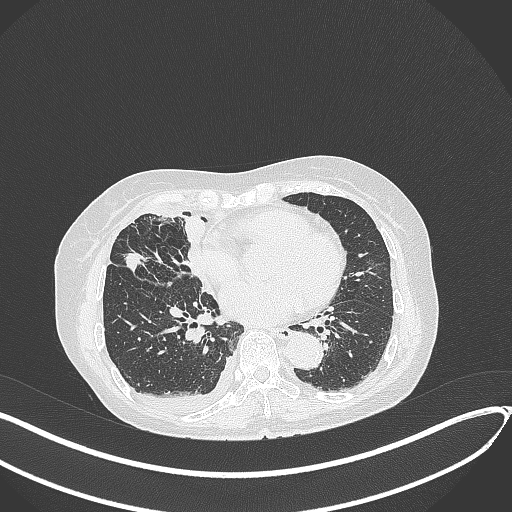
Chest CT, one axial slice; position 163 of 418 along the scan axis; reconstruction kernel B70f; 120 kVp; lung window (W 1500 / L -600 HU); 1 mm slice thickness; 512 × 512 image matrix, field of view 400 × 400 mm. Patient: female, 75 years. Case-level facts recorded for this patient, not image findings: clinical TNM (as recorded): T2a N3 M0.
Annotated regions visible in this slice (rectangle marked by the reading radiologist):
- lung tumour (recorded histology: adenocarcinoma): box from (x=123, y=245) to (x=148, y=278) px